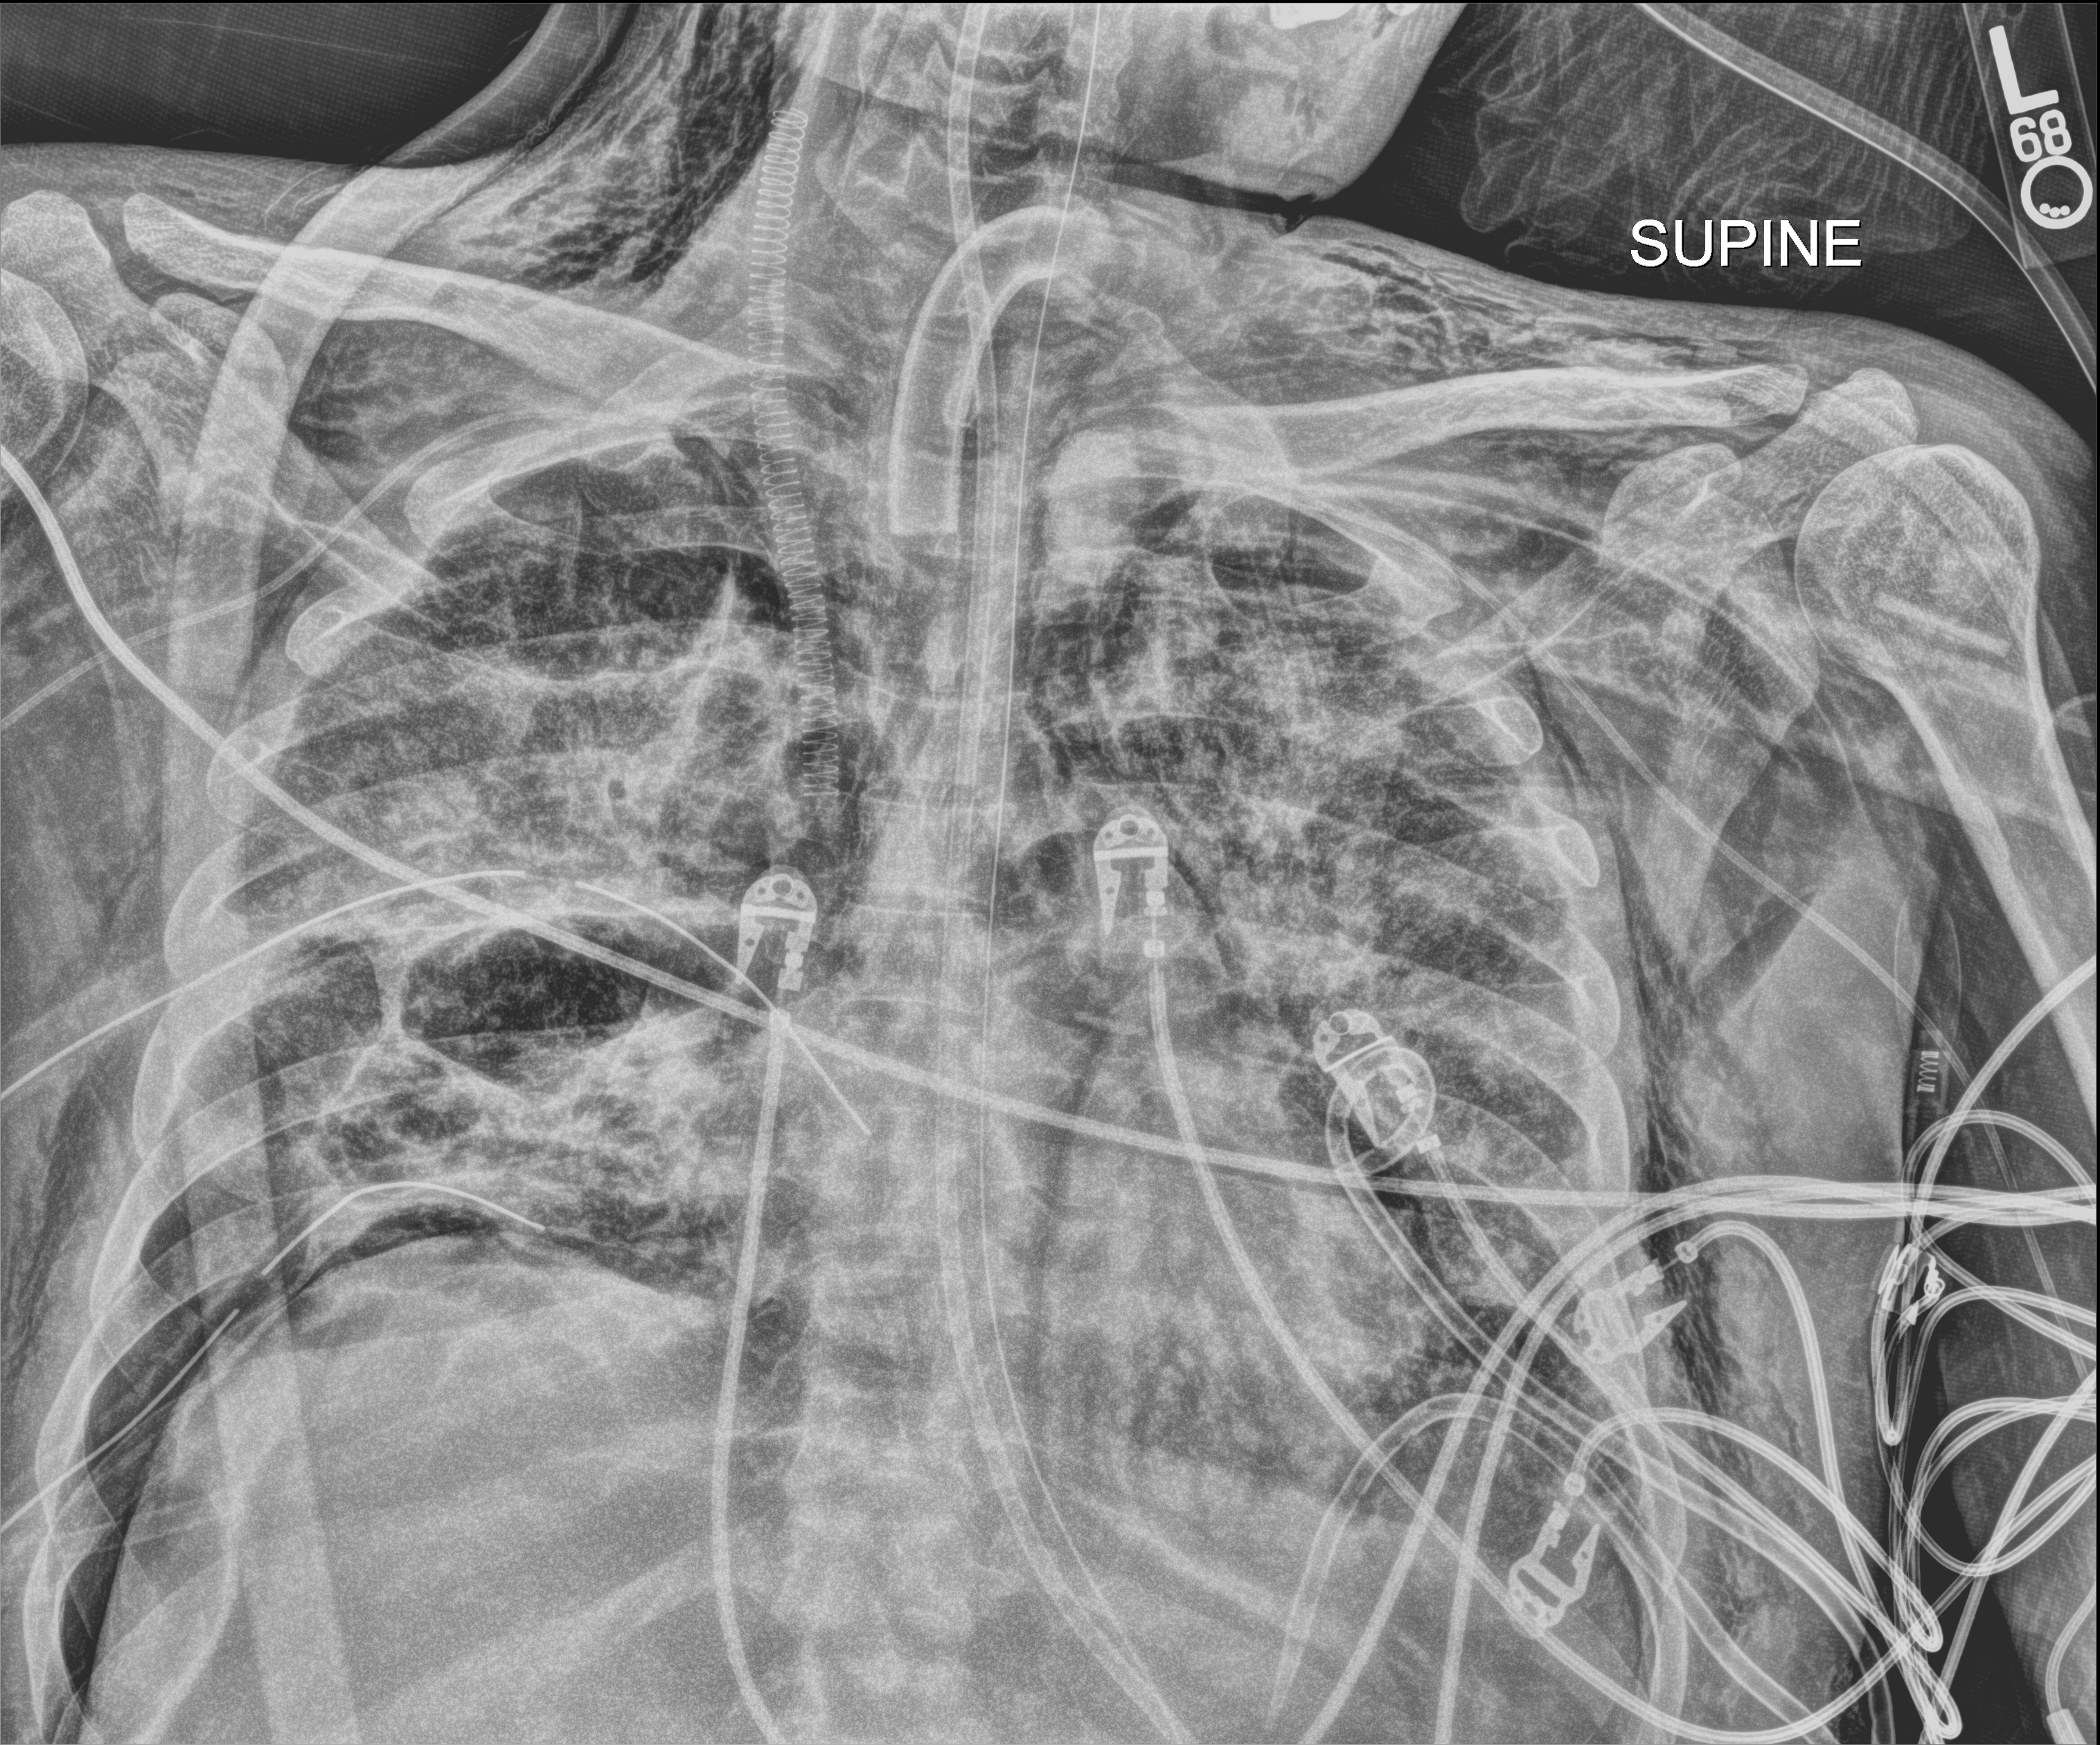
Chest X-ray, anteroposterior (AP) projection. Patient hospitalised with COVID-19, aged 18–59 years.
Hospital-stay facts (about this admission, not read from this image; timing relative to this image not recorded):
- mechanically ventilated during this hospital stay: yes
- length of hospital stay: 60 days